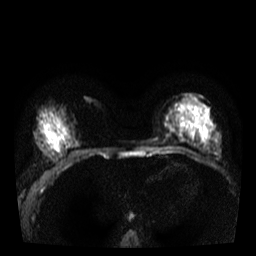
Breast MRI, one axial slice; position 17 of 40 along the scan axis; diffusion-weighted series; image 2 of 4 stored at this slice position (different b-values; order by instance number); 3 T; 256 × 256 image matrix, field of view 320 × 320 mm. Female patient.
Annotated regions visible in this slice (outlined manually by an expert reader):
- tumour on diffusion-weighted imaging: bounding box [x1, y1, x2, y2] px = [190, 112, 200, 122]